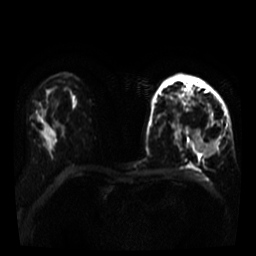
Breast MRI, one axial slice; slice 20 of 35 in the series (ordered by position); diffusion-weighted series; image 2 of 4 stored at this slice position (different b-values; order by instance number); 3 T; 256 × 256 image matrix, field of view 320 × 320 mm. Female patient.
Annotated regions visible in this slice (expert manual segmentation):
- tumour on diffusion-weighted imaging: bounding box (x1, y1, x2, y2) in pixels: (189, 131, 219, 159)